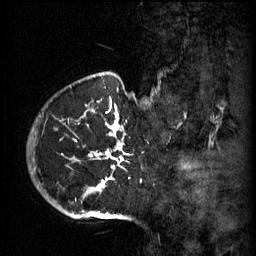
Breast MRI (dynamic contrast-enhanced), one sagittal slice; slice 50 of 60 in the series (ordered by position); 3 images stored at this slice position (order not interpretable as contrast timing); 1.5 T; TE 4.2 ms, TR 11 ms; 2 mm slice thickness; 256 × 256 image matrix, field of view 200 × 200 mm. Patient: female, 51 years.
Annotated regions visible in this slice (semi-automatic segmentation, software-assisted and operator-edited):
- analysis volume of interest (the breast-tissue region the enhancement analysis was run in; not a lesion): bounding box <48,82,158,197> (left, top, right, bottom; pixels)
- tumour enhancement mask (voxels above the 70 % enhancement threshold inside the analysis volume of interest): <74,116,124,189>